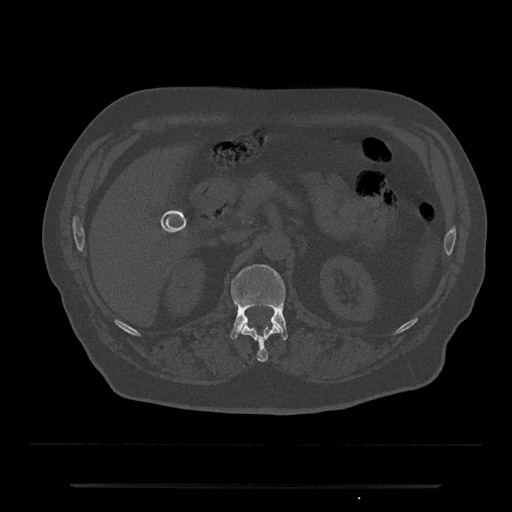
CT including the spine, one axial slice; slice 557 of 797 in the series (ordered by position); 120 kVp; bone window (W 1800 / L 400 HU); 512 × 512 image matrix, field of view 434 × 434 mm. Male patient, age 80 years. Case-level facts recorded for this patient, not image findings: primary cancer: prostate; vertebrae with lytic lesions (as recorded): L1, T11.
Annotated regions visible in this slice (semi-automatic segmentation, software-assisted and operator-edited):
- L1 vertebra: box from (x=230, y=265) to (x=288, y=340) px
- T12 vertebra: (x=241, y=324)–(x=280, y=362)